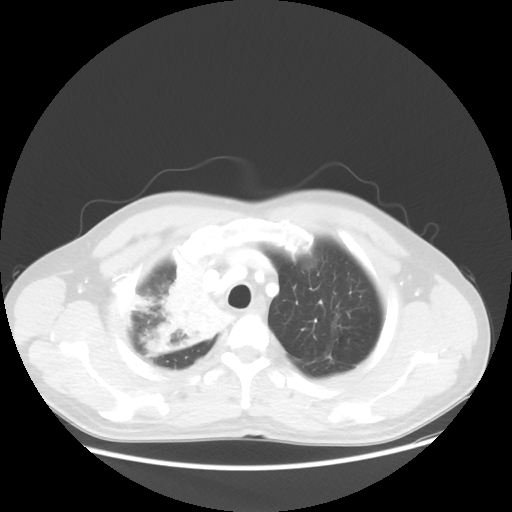
Chest CT, one axial slice. Slice 45 of 56 in the series (ordered by position). Reconstruction kernel STANDARD. 100 kVp. Lung window (W 1500 / L -600 HU). 512 × 512 image matrix. Male patient, age 60 years. From the clinical record (not read from this slice): clinical TNM (as recorded): T2a N1 M0.
Outlined on this slice (rectangle marked by the reading radiologist):
- lung tumour (recorded histology: squamous cell carcinoma): bounding box (x1, y1, x2, y2) in pixels: (138, 255, 228, 355)